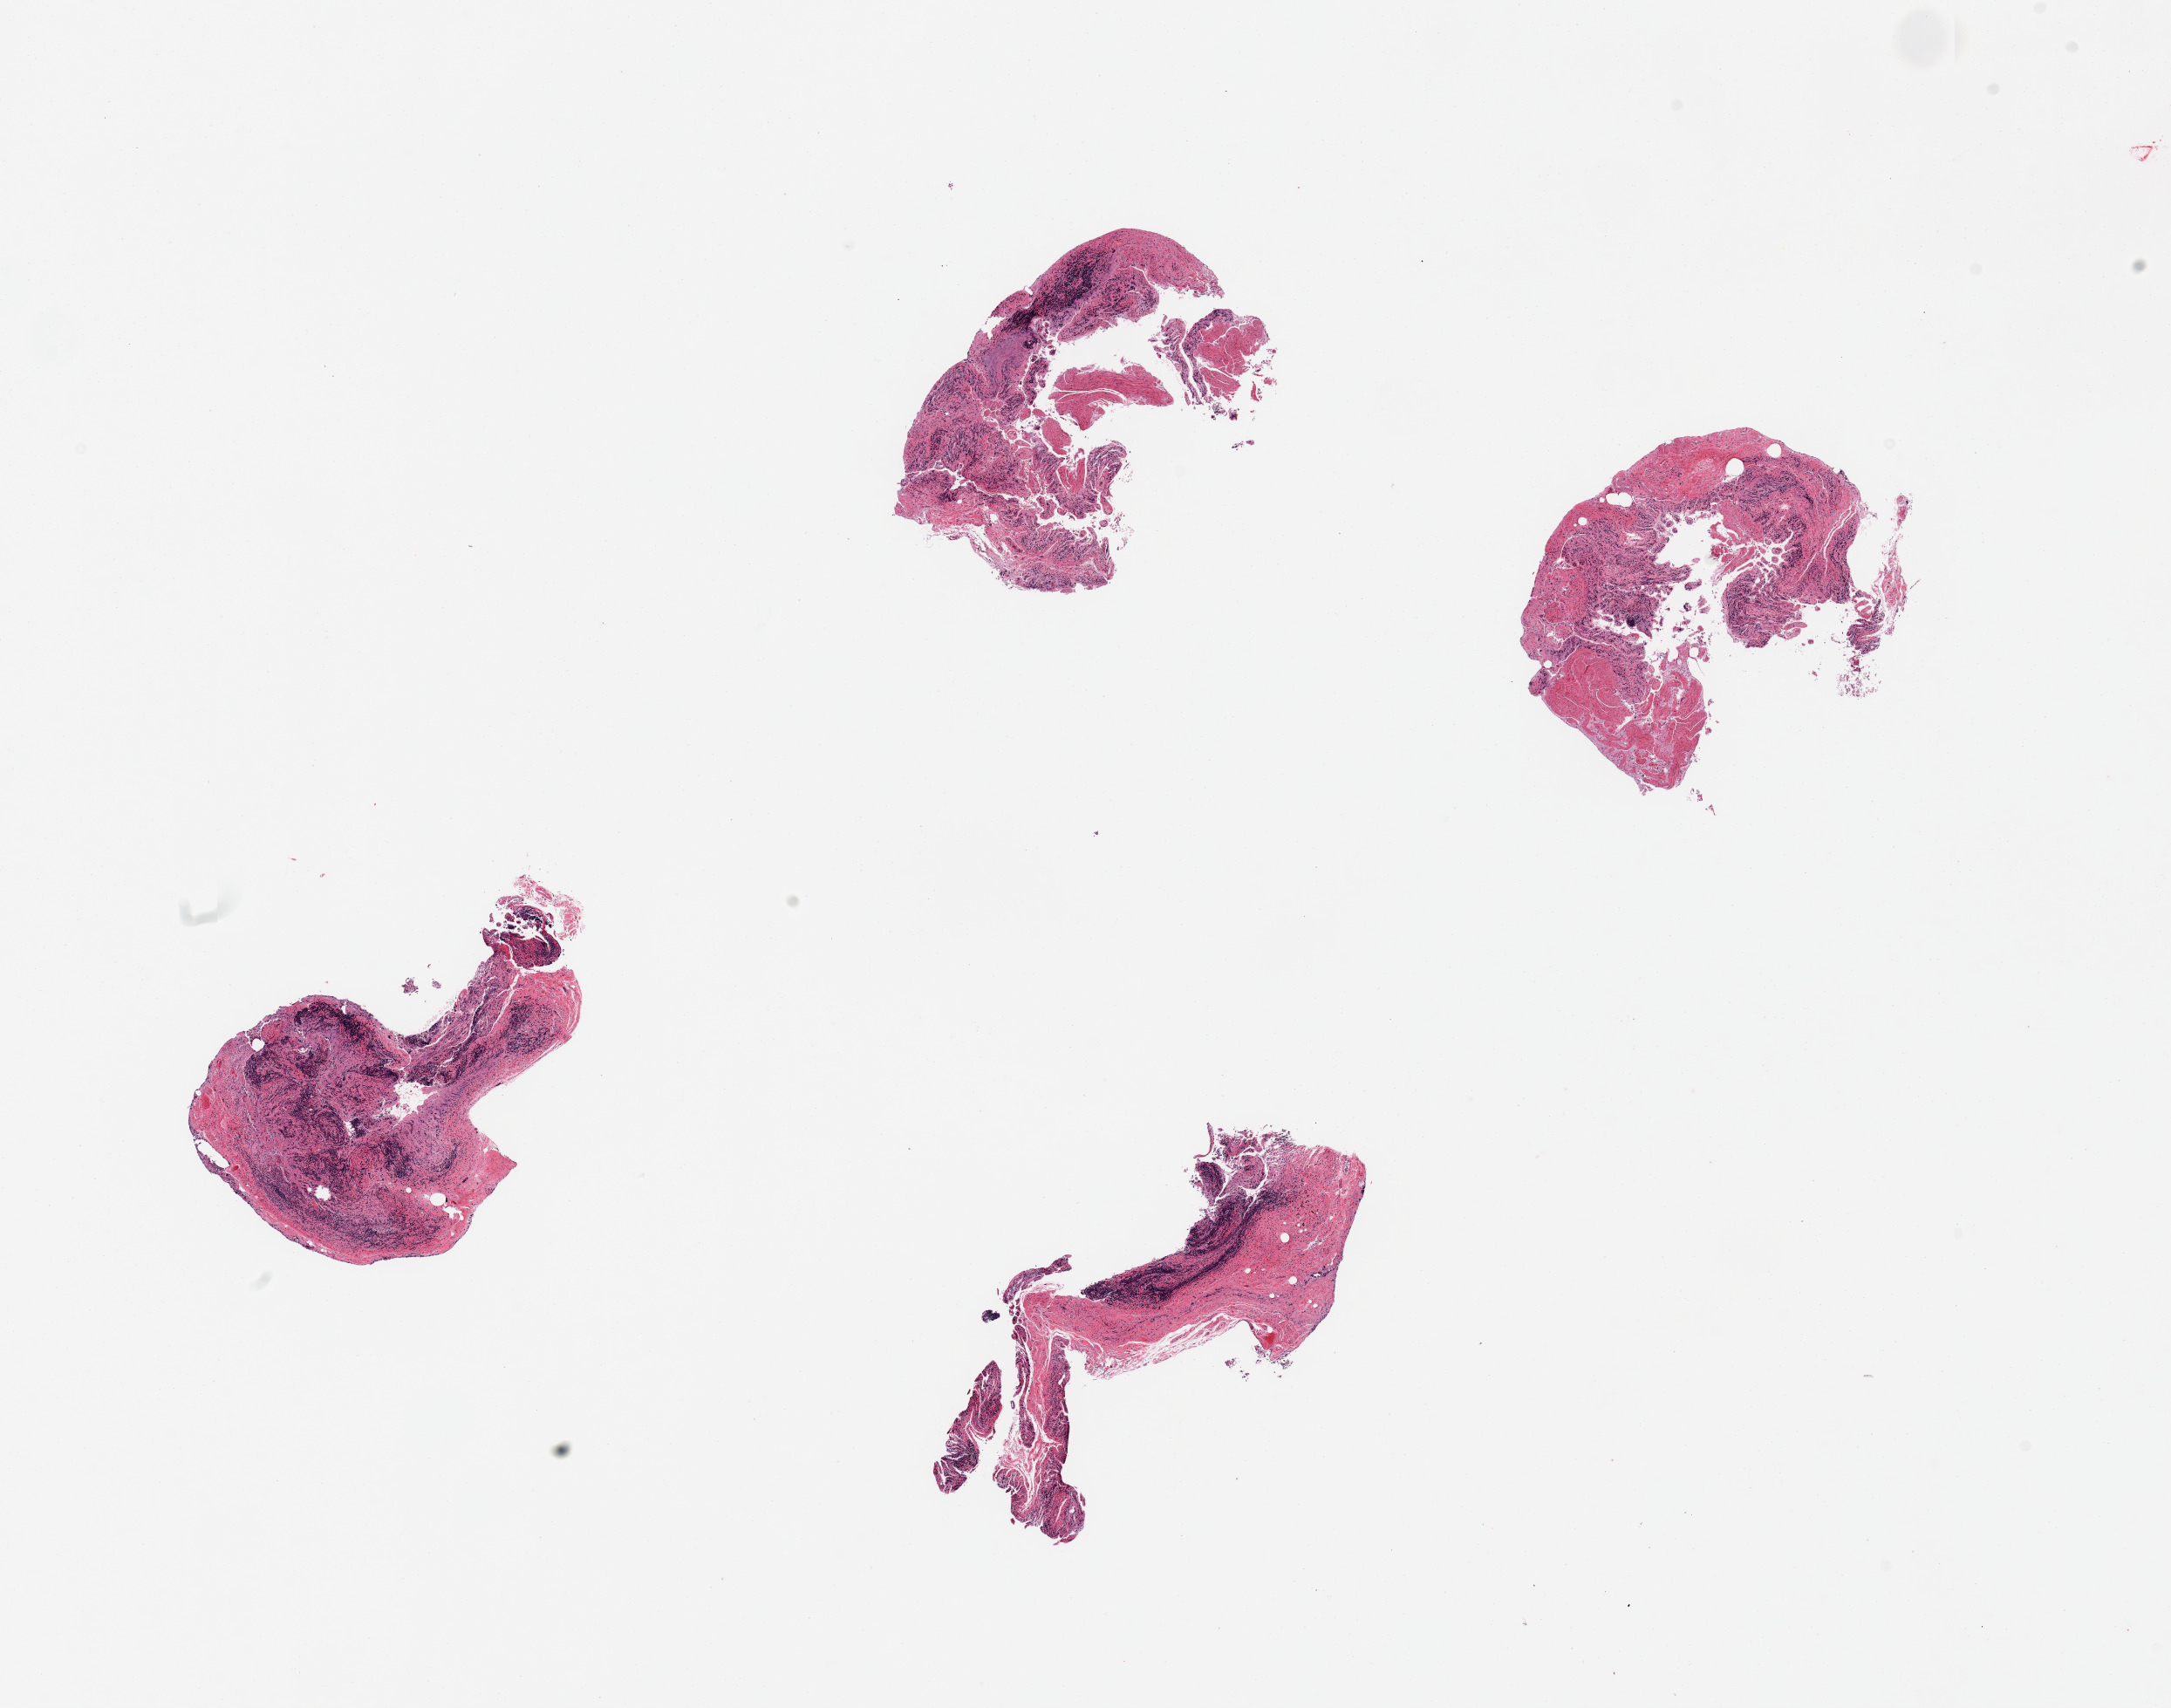
Whole-slide image, H&E stain — whole scanned area (about 19.7 x 15.5 mm, from a 20x scan) shown as a low-resolution overview. PAXgene-fixed, paraffin-embedded tissue. Target tissue: ileum. Tissue donor sample. Donor: male.
* pathologist's review note for this sample: 4 pieces, mucosa autolyzed; residual lymphoid aggregates; ~15% total tissue